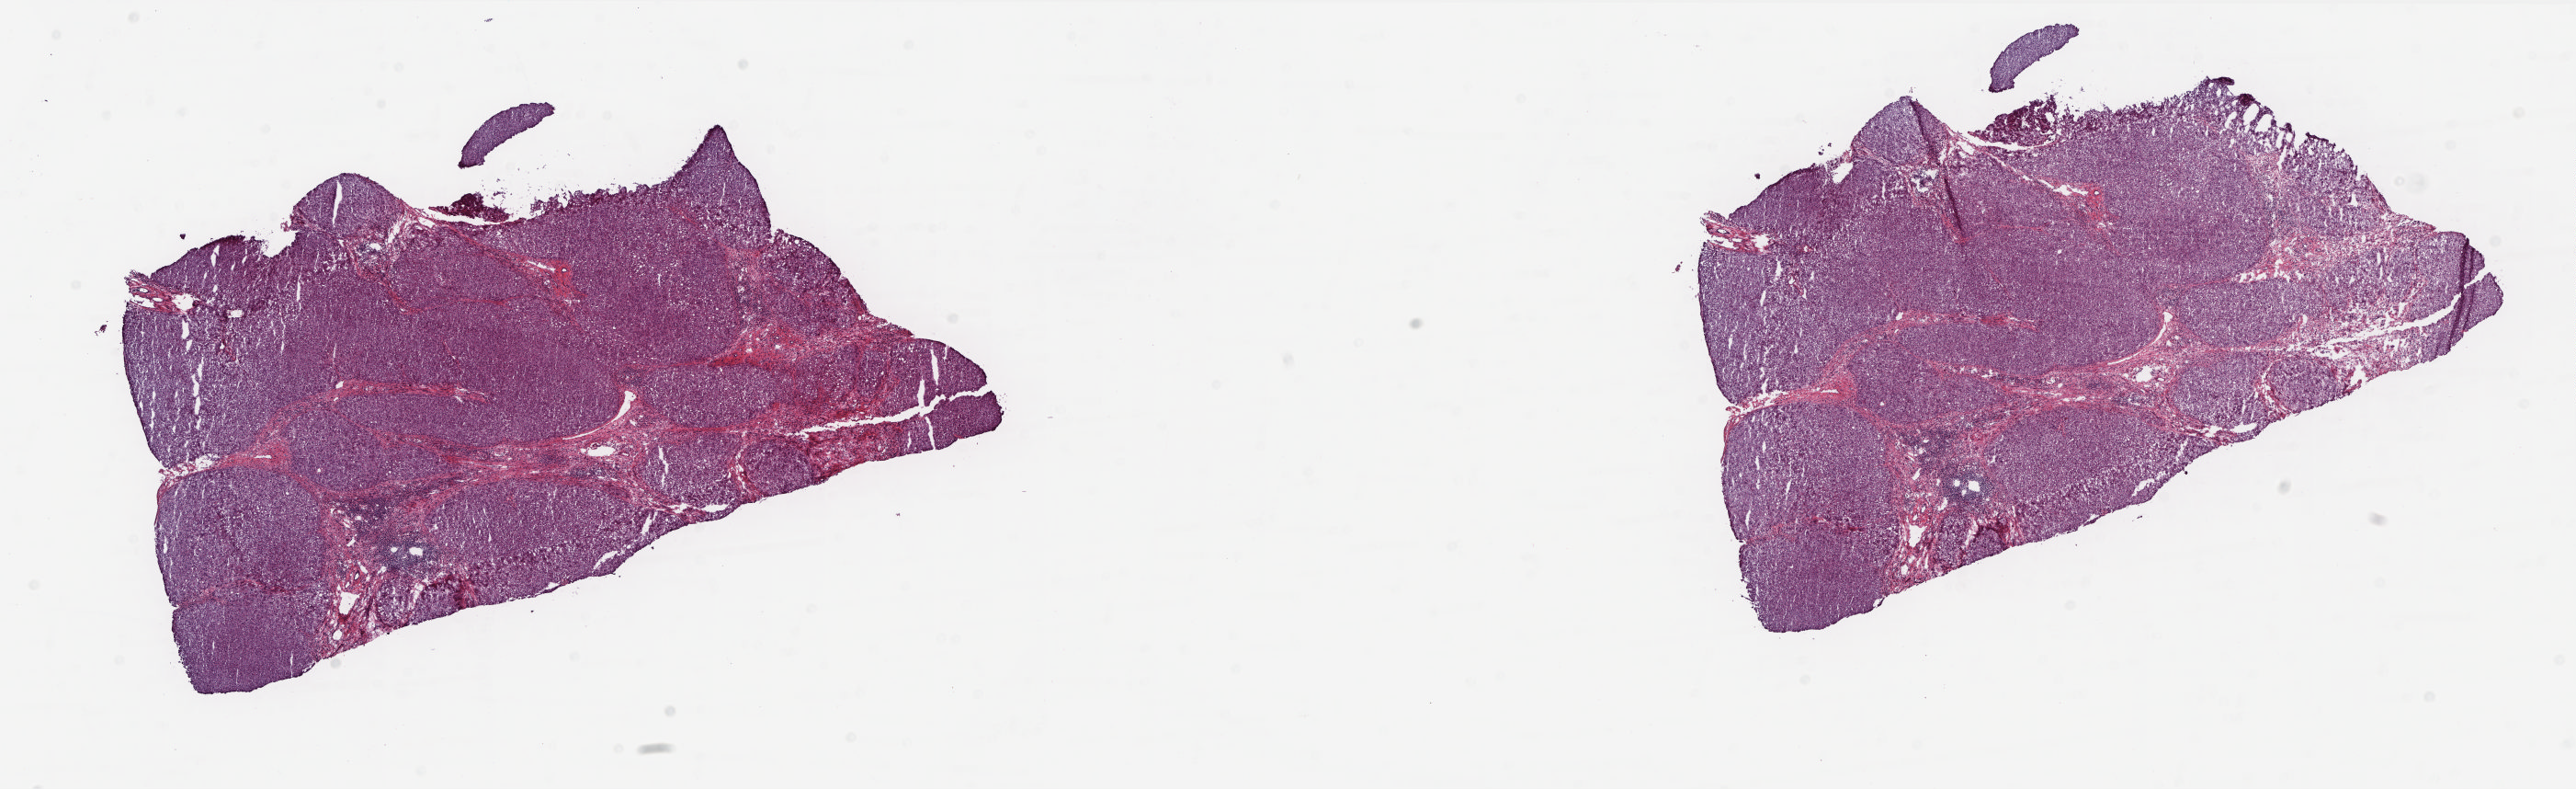
Digitized Hematoxylin and eosin (H&E) stained tissue section (whole slide), low-resolution overview of the scanned area, about 22.6 x 6.9 mm, frozen section from the top of the tissue portion, solid tissue normal (non-tumour tissue) sample from the liver. Male patient; age at initial diagnosis 64 years. Composition of this section per pathologist review: tumour cells 0%, tumour nuclei 0%, normal cells 80%, stromal cells 20%, necrosis 0%. Inflammatory infiltration, as recorded: lymphocyte infiltration 4%, monocyte infiltration 1%, neutrophil infiltration 0%.
* this section: solid tissue normal sample (biorepository sample class)
* patient diagnosis: Hepatocellular carcinoma, NOS